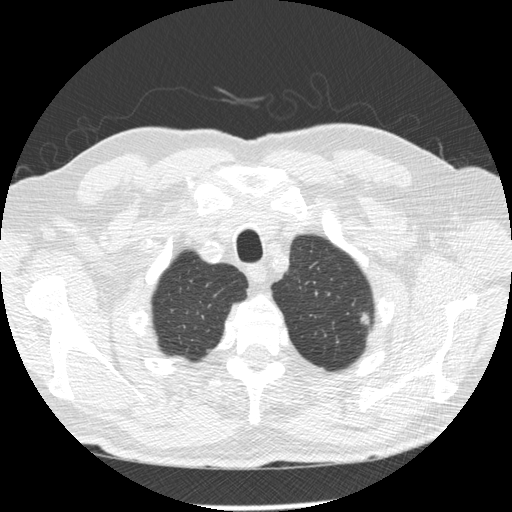
Axial slice from a low-dose chest CT screening exam. Third screening round (two years after baseline). Lung window (W 1500 / L -600 HU). 2.5 mm slice thickness. 120 kVp. Slice 25 of 258 in the series. 512 × 512 image matrix, field of view 360 × 360 mm. Male, age 73 years at enrolment. Former smoker at enrolment.
Expert reader's lesion annotation, box from (x=351, y=299) to (x=389, y=338) px. Reader record for this screening exam (exam-level; its link to the box is not recorded): non-calcified nodule or mass ≥4 mm, left upper lobe, 8 × 7 mm, poorly defined margins, mixed attenuation, pre-existing on the prior screen: no.